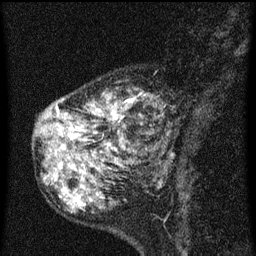
Breast MRI (dynamic contrast-enhanced), one sagittal slice. Slice 21 of 60 in the series (ordered by position). Dynamic contrast-enhanced series, image 2 of 3 at this slice position (ordered by acquisition). 1.5 T. TE 4.2 ms, TR 8 ms. 256 × 256 image matrix. Female patient, age 55 years.
Outlined on this slice (semi-automatic segmentation, software-assisted and operator-edited):
- analysis volume of interest (the breast-tissue region the enhancement analysis was run in; not a lesion): bounding box (x1, y1, x2, y2) in pixels: (42, 76, 179, 155)
- tumour enhancement mask (voxels above the 70 % enhancement threshold inside the analysis volume of interest): (57, 94, 174, 155)